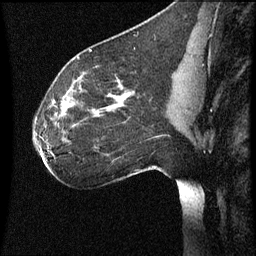
Breast MRI (dynamic contrast-enhanced), one sagittal slice. Position 38 of 60 along the scan axis. Dynamic contrast-enhanced series, image 2 of 3 at this slice position (ordered by acquisition). 1.5 T. TE 4.2 ms, TR 8.9 ms. 2 mm slice thickness. 256 × 256 image matrix, field of view 200 × 200 mm. Patient: female, 35 years. Case-level facts recorded for this patient, not image findings: setting: breast cancer imaged before/during neoadjuvant chemotherapy; receptor status: HER2-positive.
Structures marked on this image (semi-automatically segmented with operator editing):
- analysis volume of interest (the breast-tissue region the enhancement analysis was run in; not a lesion): bounding box [x1, y1, x2, y2] px = [31, 66, 177, 177]
- tumour enhancement mask (voxels above the 70 % enhancement threshold inside the analysis volume of interest): [66, 94, 126, 109]